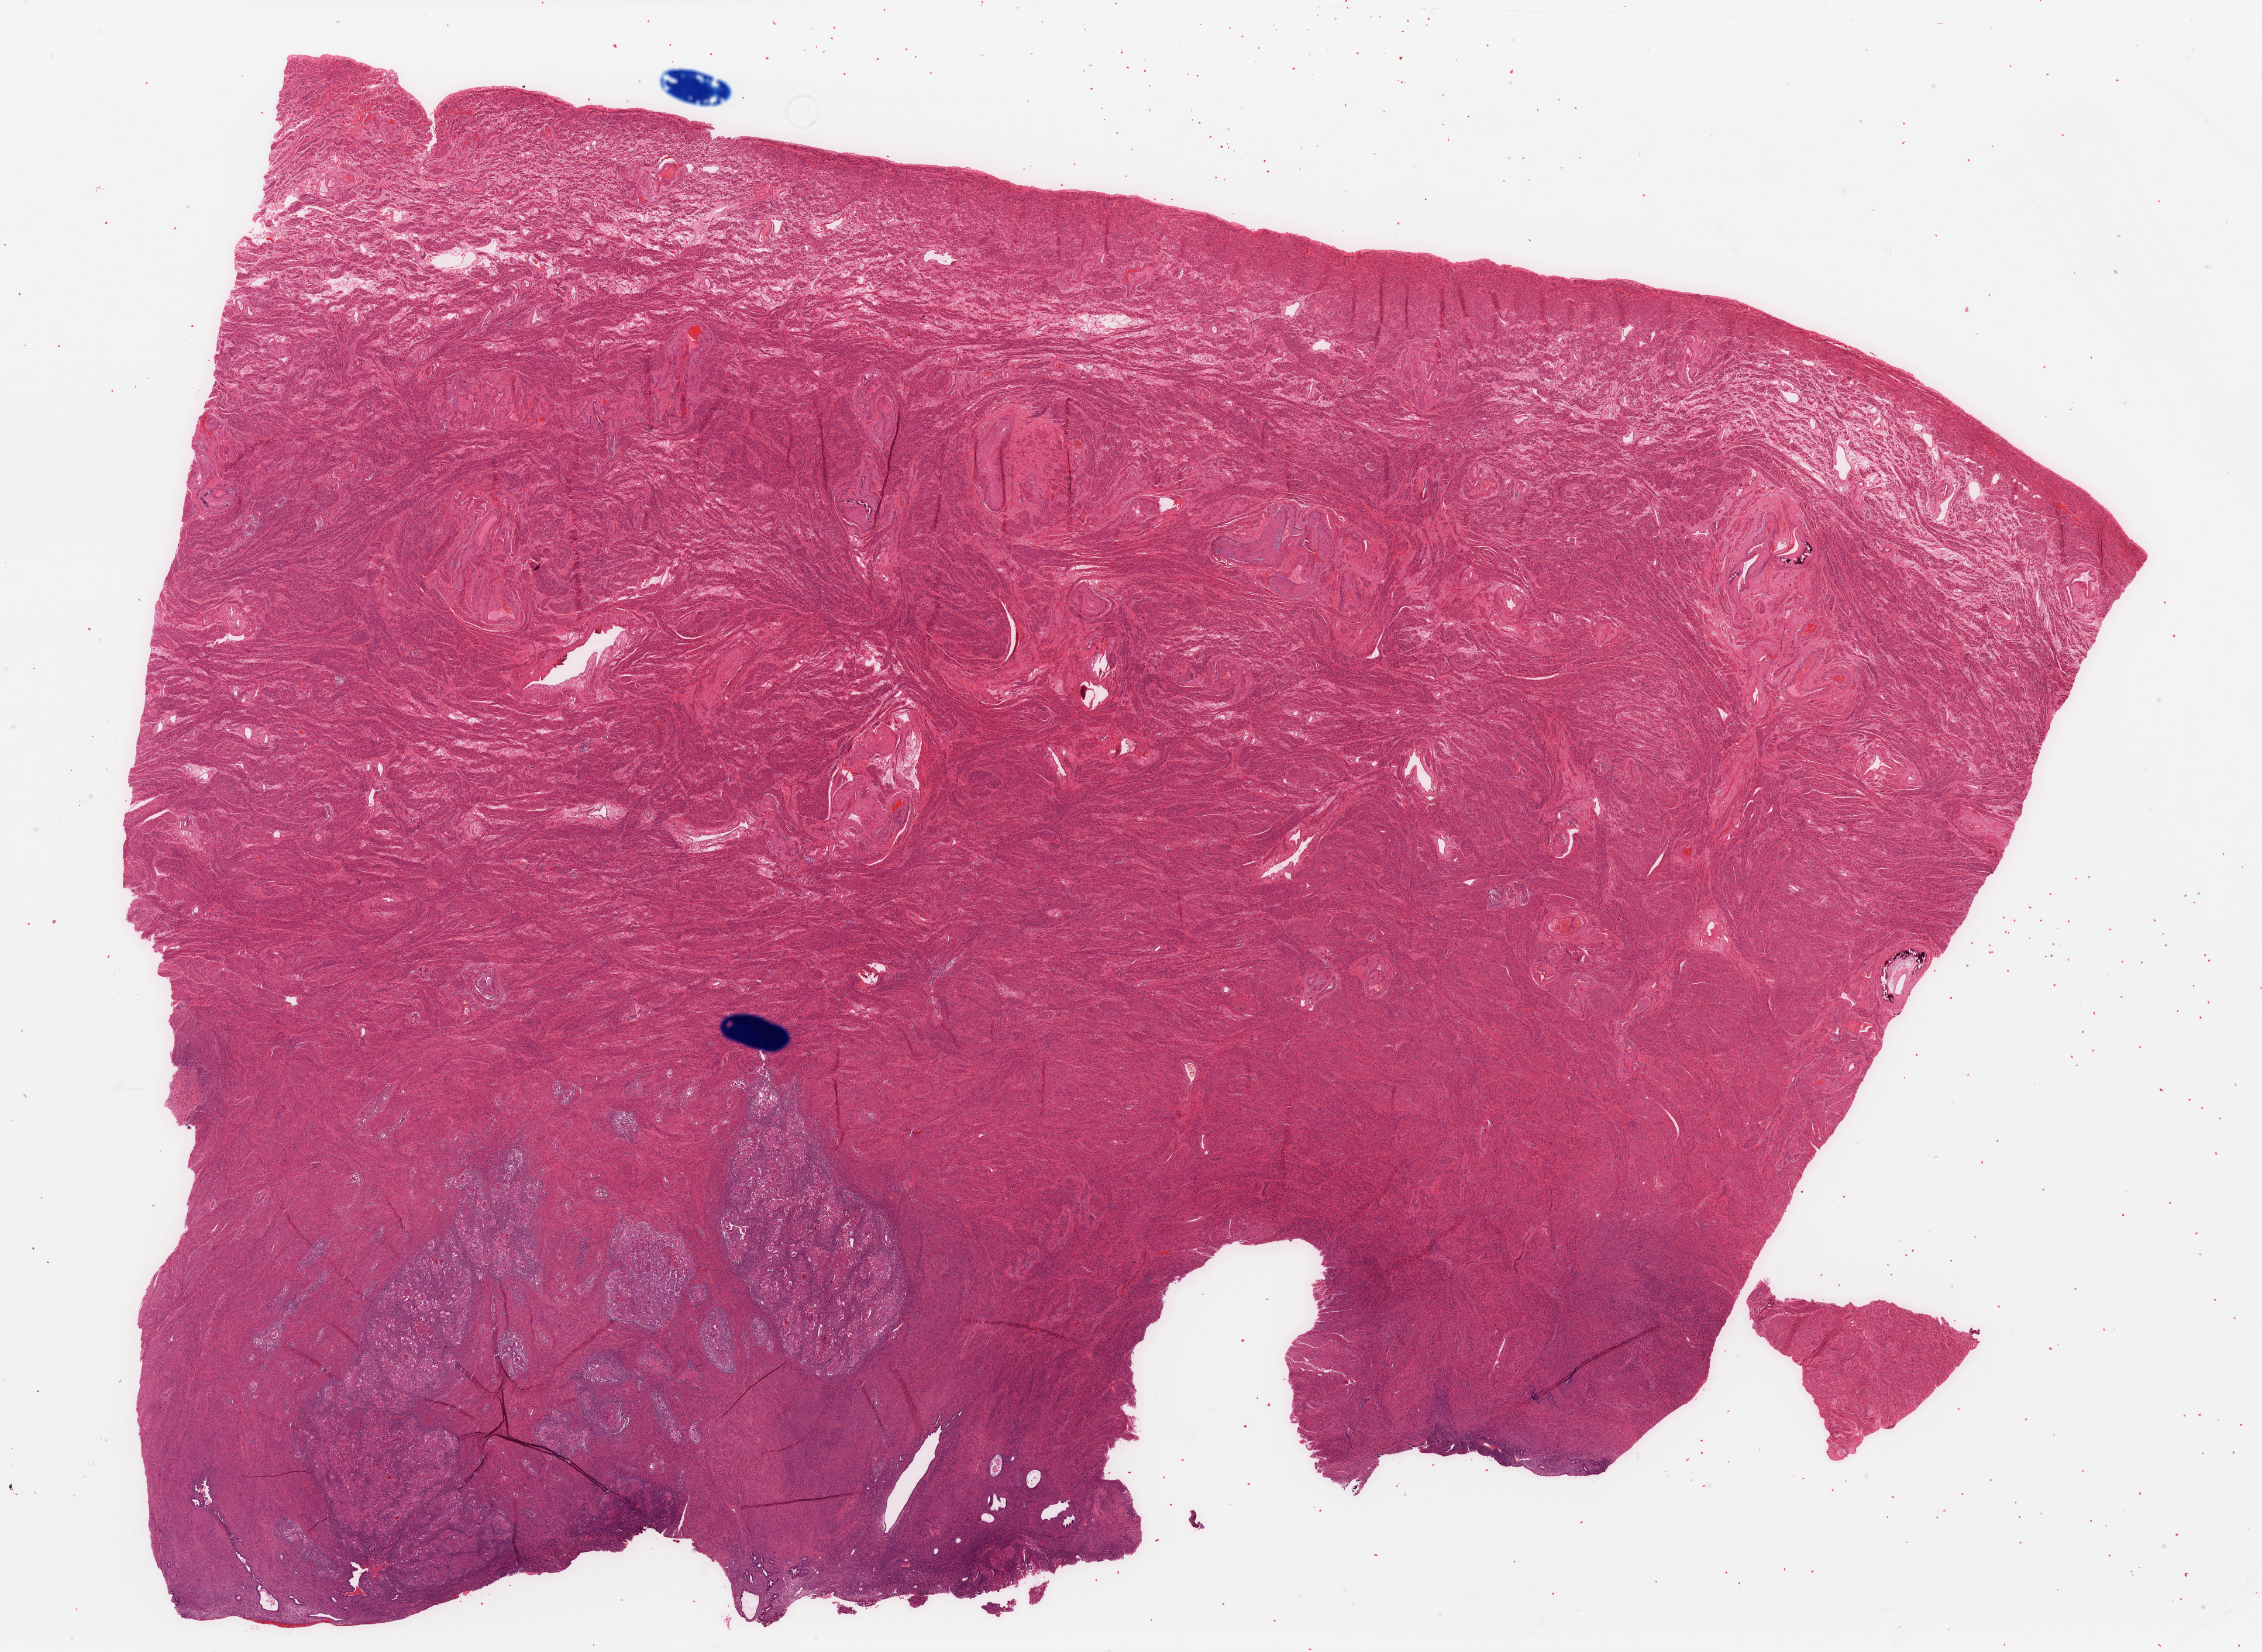
Digitized H&E tissue section (whole slide), low-resolution overview of the scanned area, about 30.5 x 22.3 mm (slide scanned at 40x), FFPE section, primary tumour sample from the uterus. Patient: female, age at initial diagnosis 82 years. Histologic grade: G3 (poorly differentiated).
Histologic diagnosis: Endometrioid adenocarcinoma, NOS (endometrium). FIGO stage: IB.